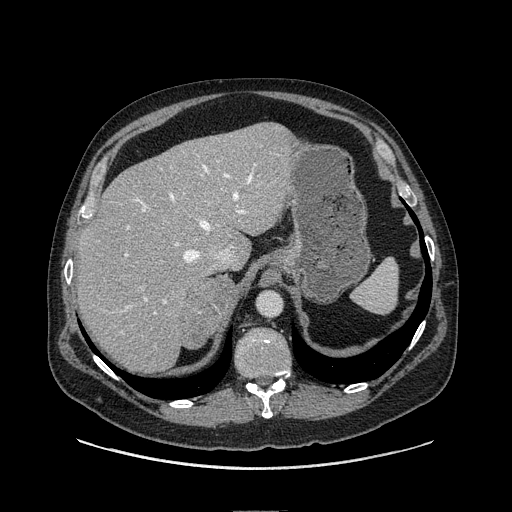
Contrast-enhanced abdominal CT, one axial slice. Position 83 of 149 along the scan axis. Soft-tissue window (W 400 / L 40 HU). 1.25 mm slice thickness. 512 × 512 image matrix, field of view 440 × 440 mm. Male patient. From the clinical record (not read from this slice): diagnosis: adrenocortical carcinoma; tumour side: right adrenal; tumour size at pathology: 7.5 cm; Ki-67 index: 15 %; stage (as recorded): 2.
Structures marked on this image (semi-automatically segmented with operator editing):
- mass: box from (x=186, y=275) to (x=236, y=347) px